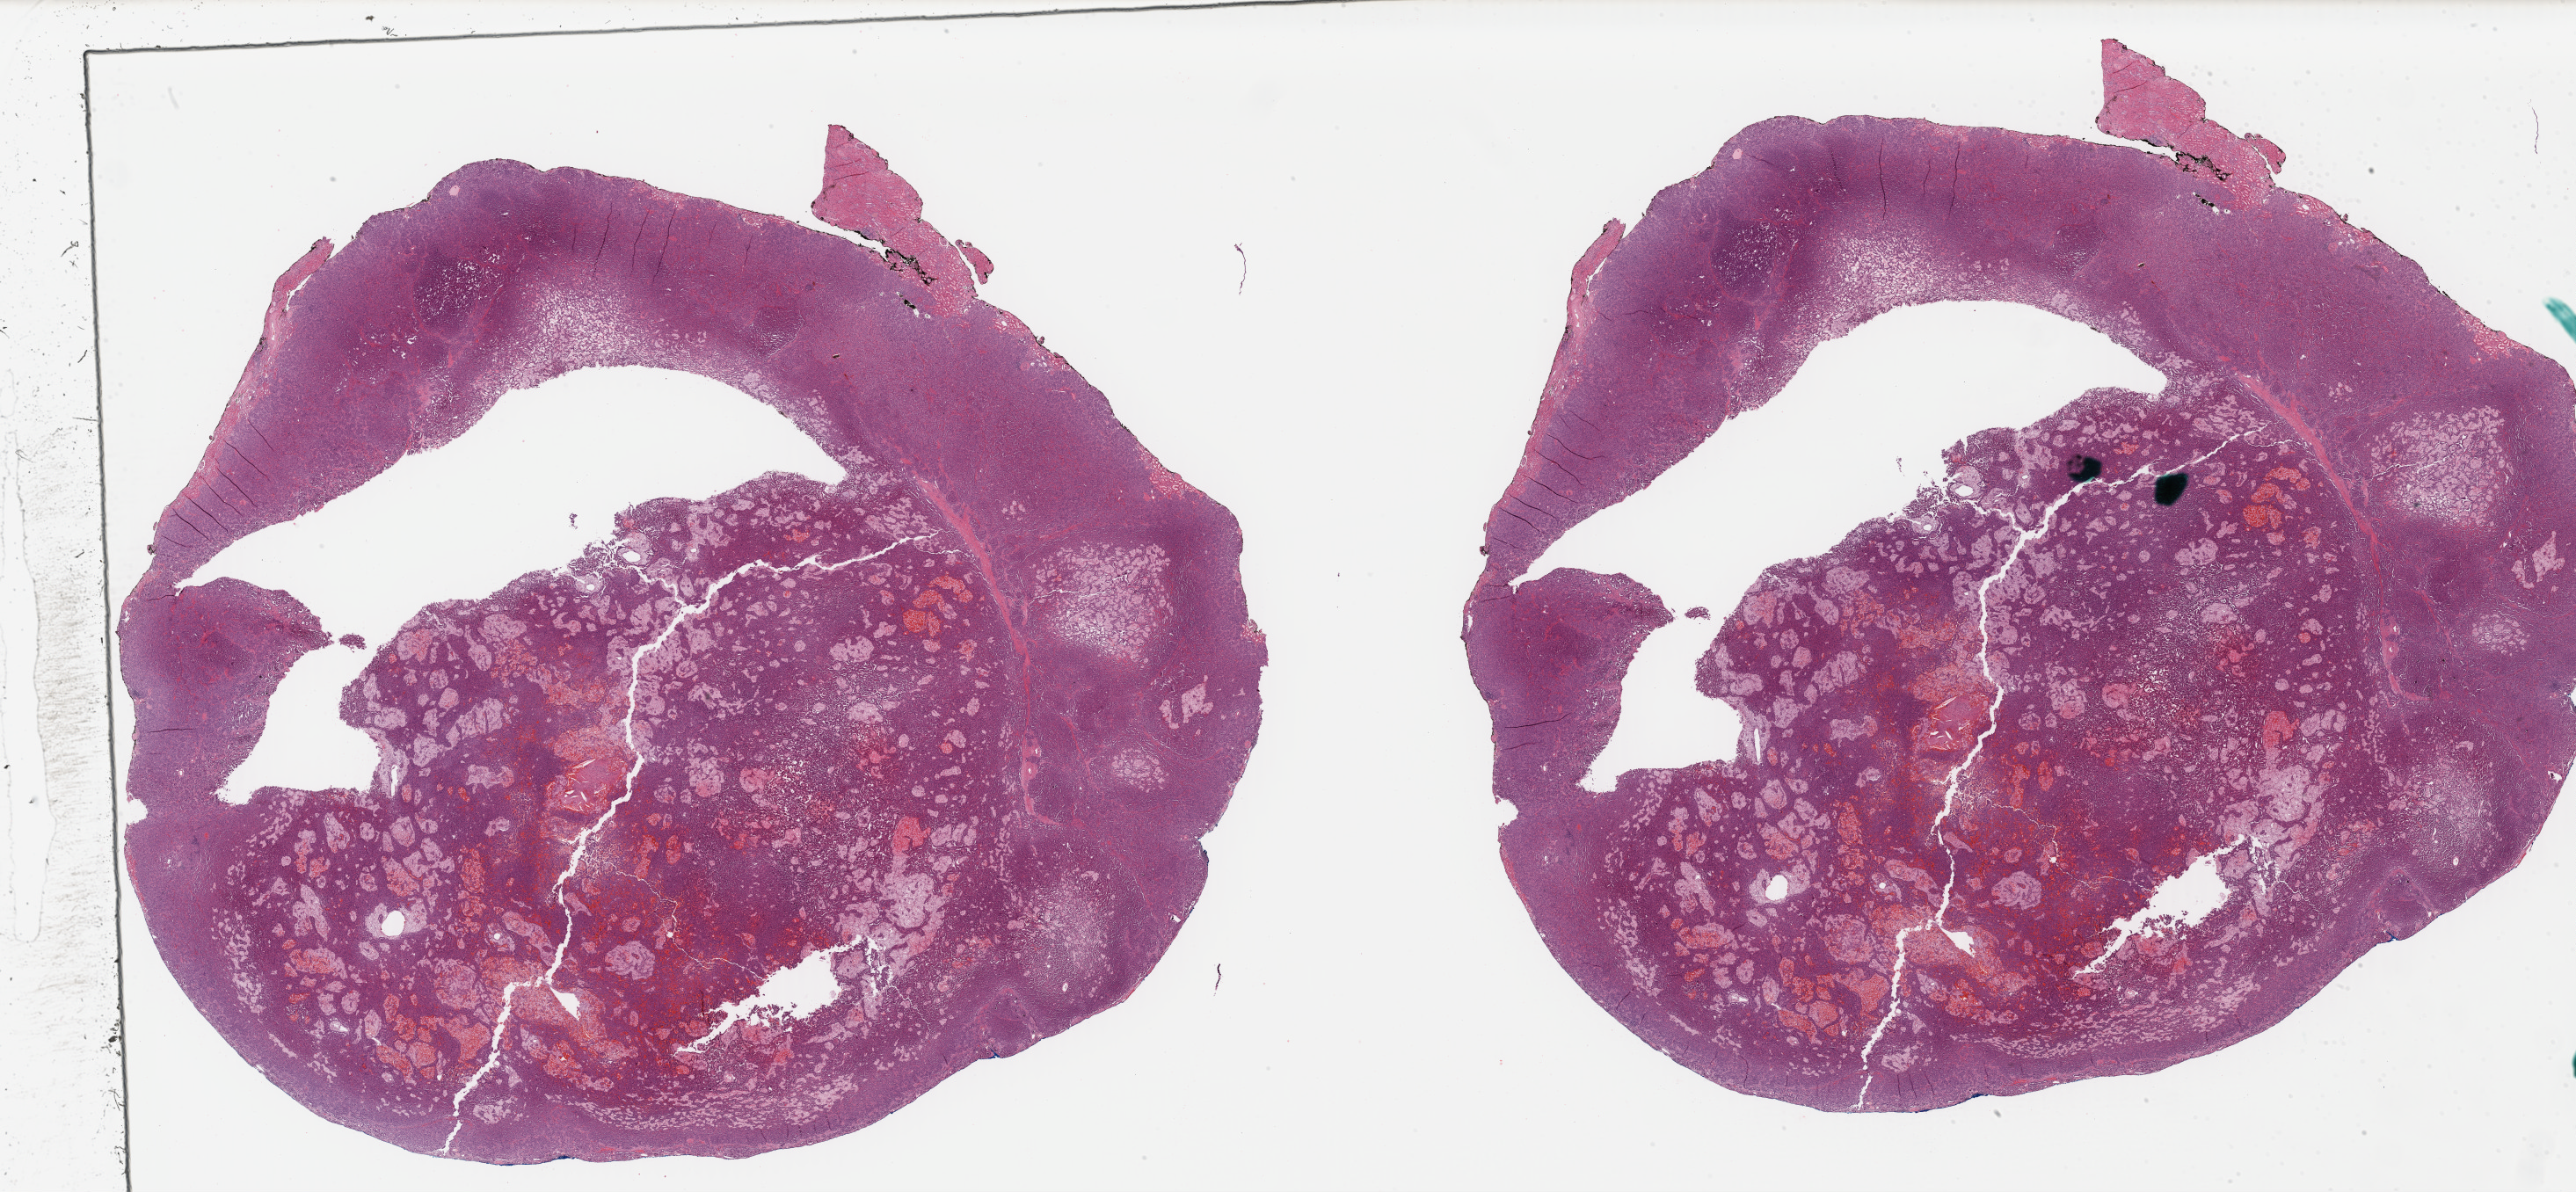
Whole-slide histology image, H&E — low-resolution overview of the scanned area, about 46.1 x 21.3 mm; FFPE section; primary tumour sample from the kidney. Male, age 62 years at initial diagnosis.
• AJCC pathologic stage: I (7th edition)
• pathologic diagnosis: Papillary adenocarcinoma, NOS